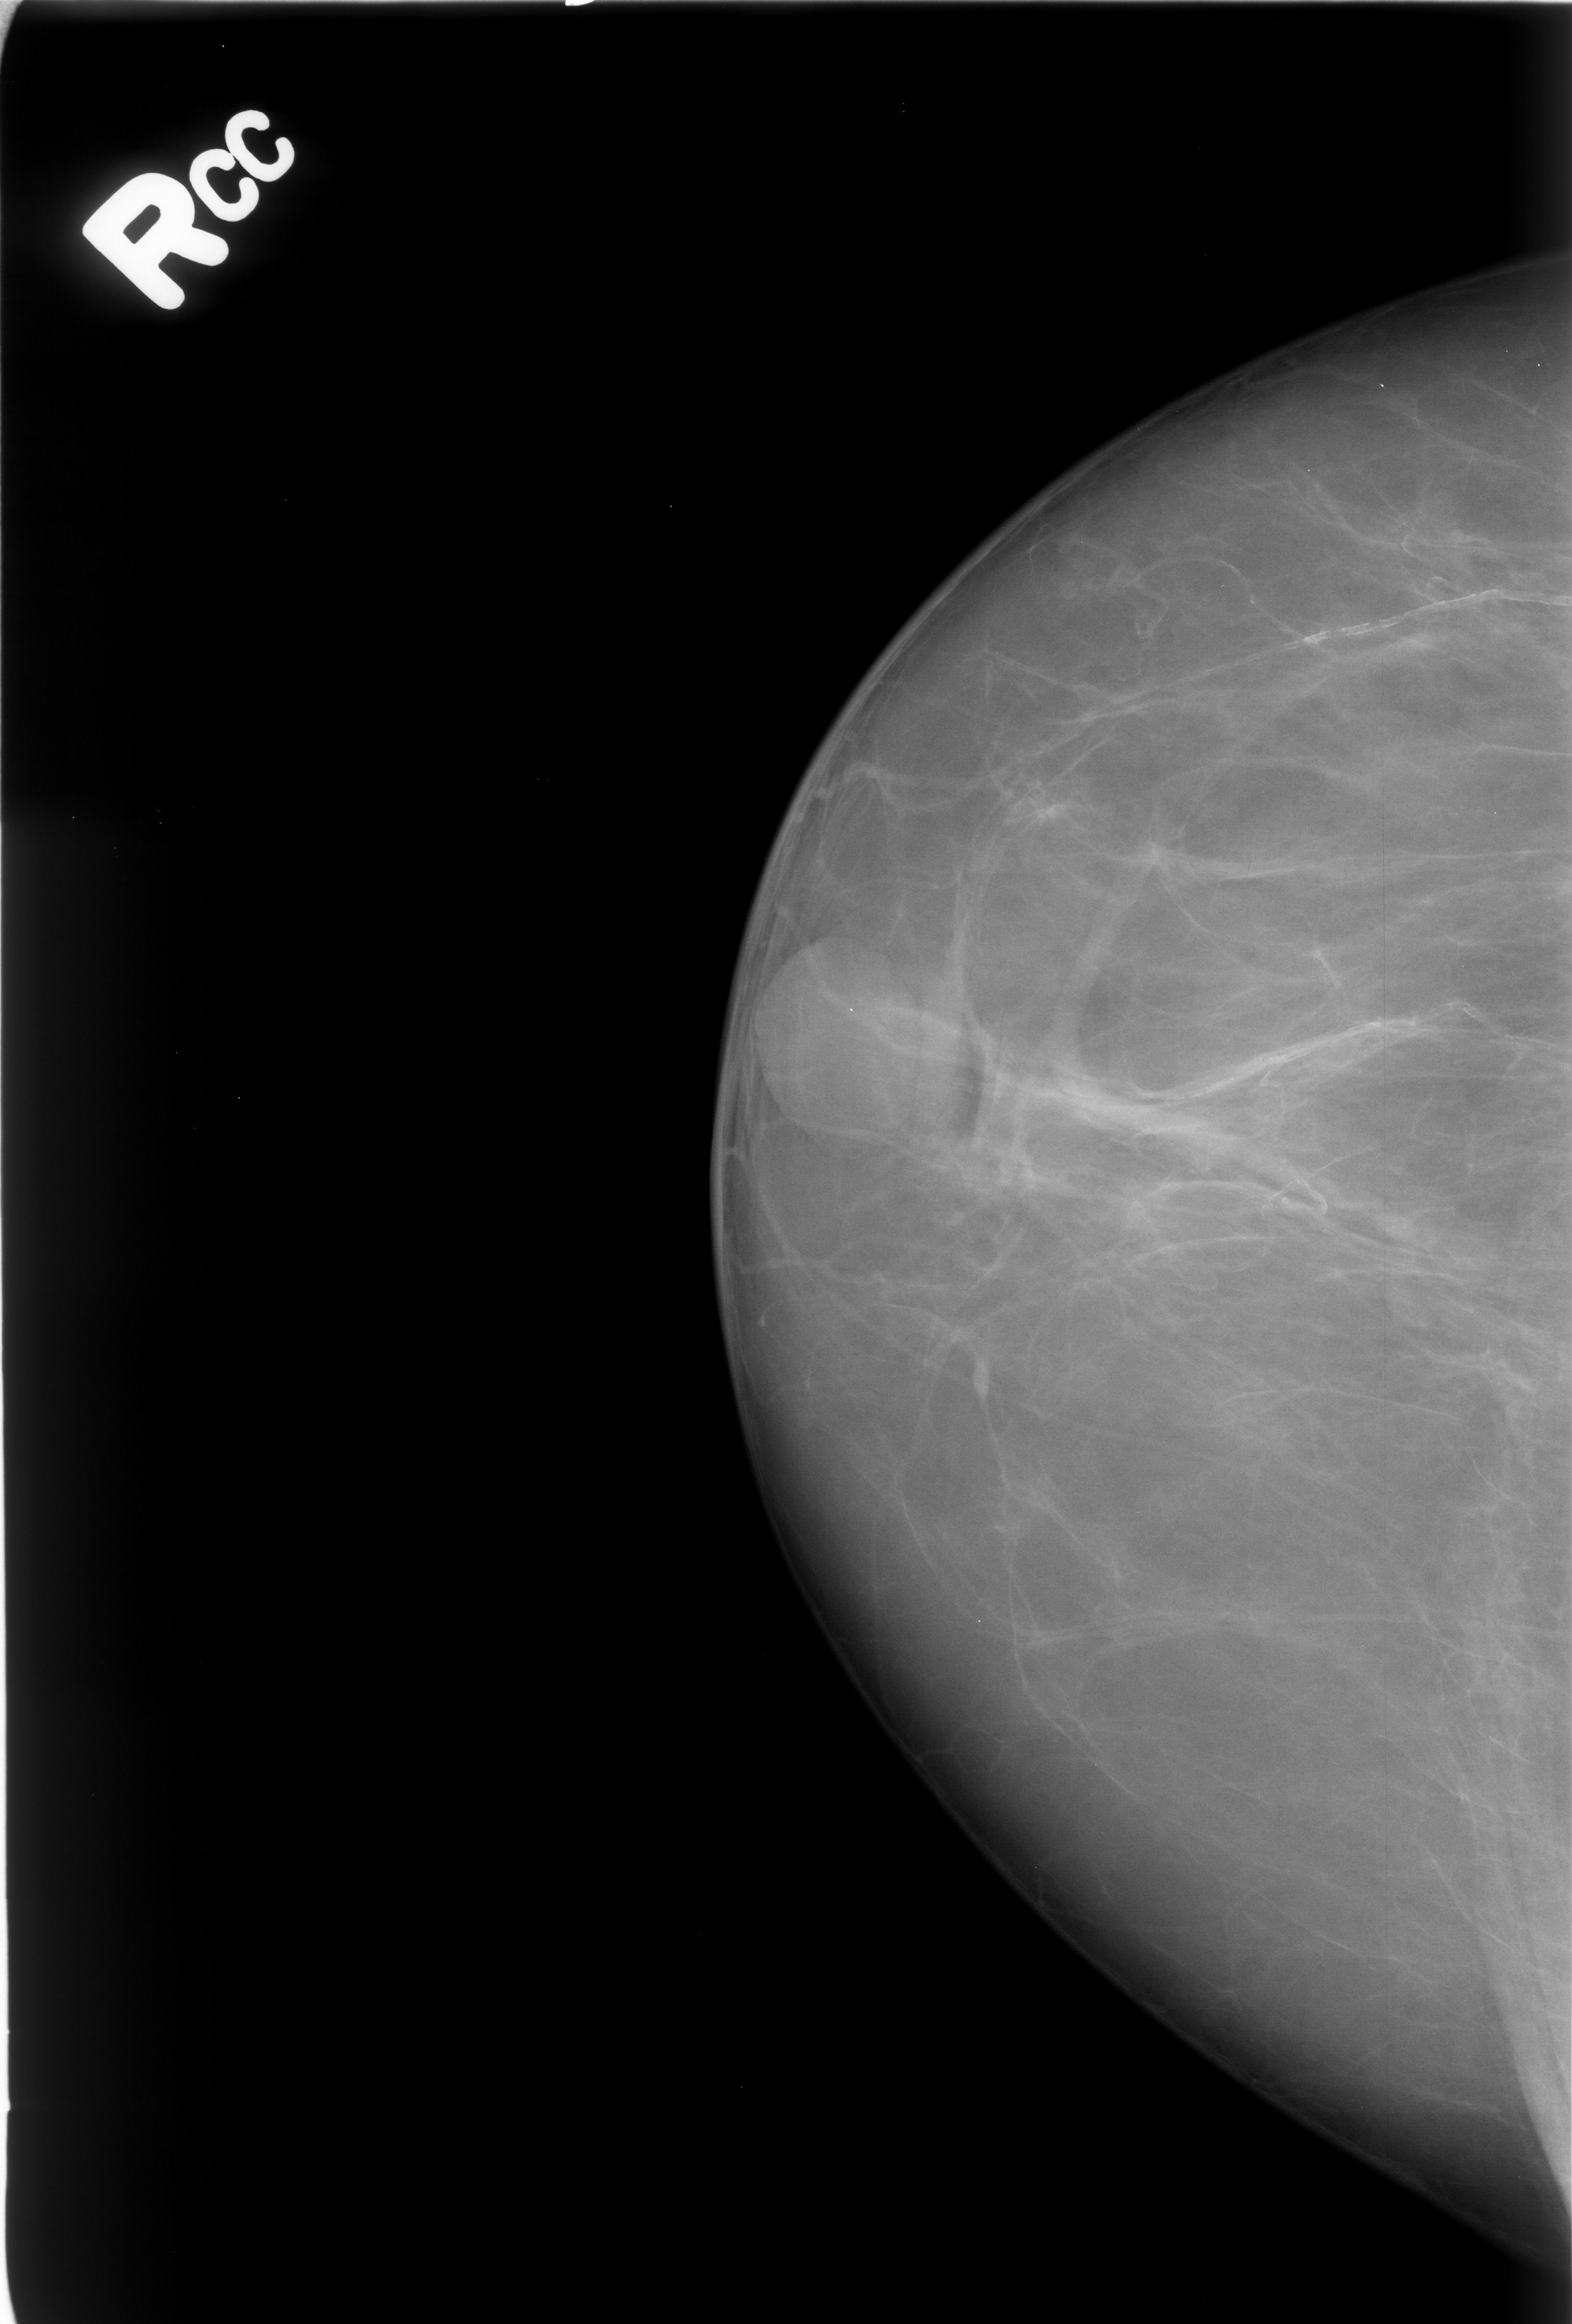
Mammogram (digitized film); right breast; CC view; BI-RADS breast density category 1 (scale 1–4).
- Abnormality record for this image: Finding 1 of 2: calcifications, morphology vascular; BI-RADS assessment category 2; subtlety rating 4 on a 1 (subtle) to 5 (obvious) scale; benign without callback (not worked up further).
- Finding 2 of 2: calcifications, morphology vascular; BI-RADS assessment category 2; subtlety rating 4 on a 1 (subtle) to 5 (obvious) scale; benign; no additional work-up was recommended (benign without callback).